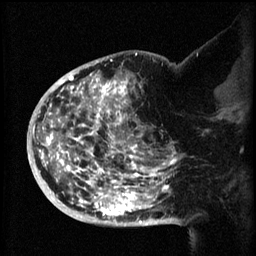
Breast MRI (dynamic contrast-enhanced), one sagittal slice; position 37 of 60 along the scan axis; 3 images stored at this slice position (order not interpretable as contrast timing); 1.5 T; TE 4.2 ms, TR 8.2 ms; 2 mm slice thickness; 256 × 256 image matrix, field of view 200 × 200 mm. Patient: female, 50 years.
Outlined on this slice (semi-automatically segmented with operator editing):
- analysis volume of interest (the breast-tissue region the enhancement analysis was run in; not a lesion): bounding box [x1, y1, x2, y2] px = [44, 72, 173, 219]
- tumour enhancement mask (voxels above the 70 % enhancement threshold inside the analysis volume of interest): [44, 72, 173, 219]